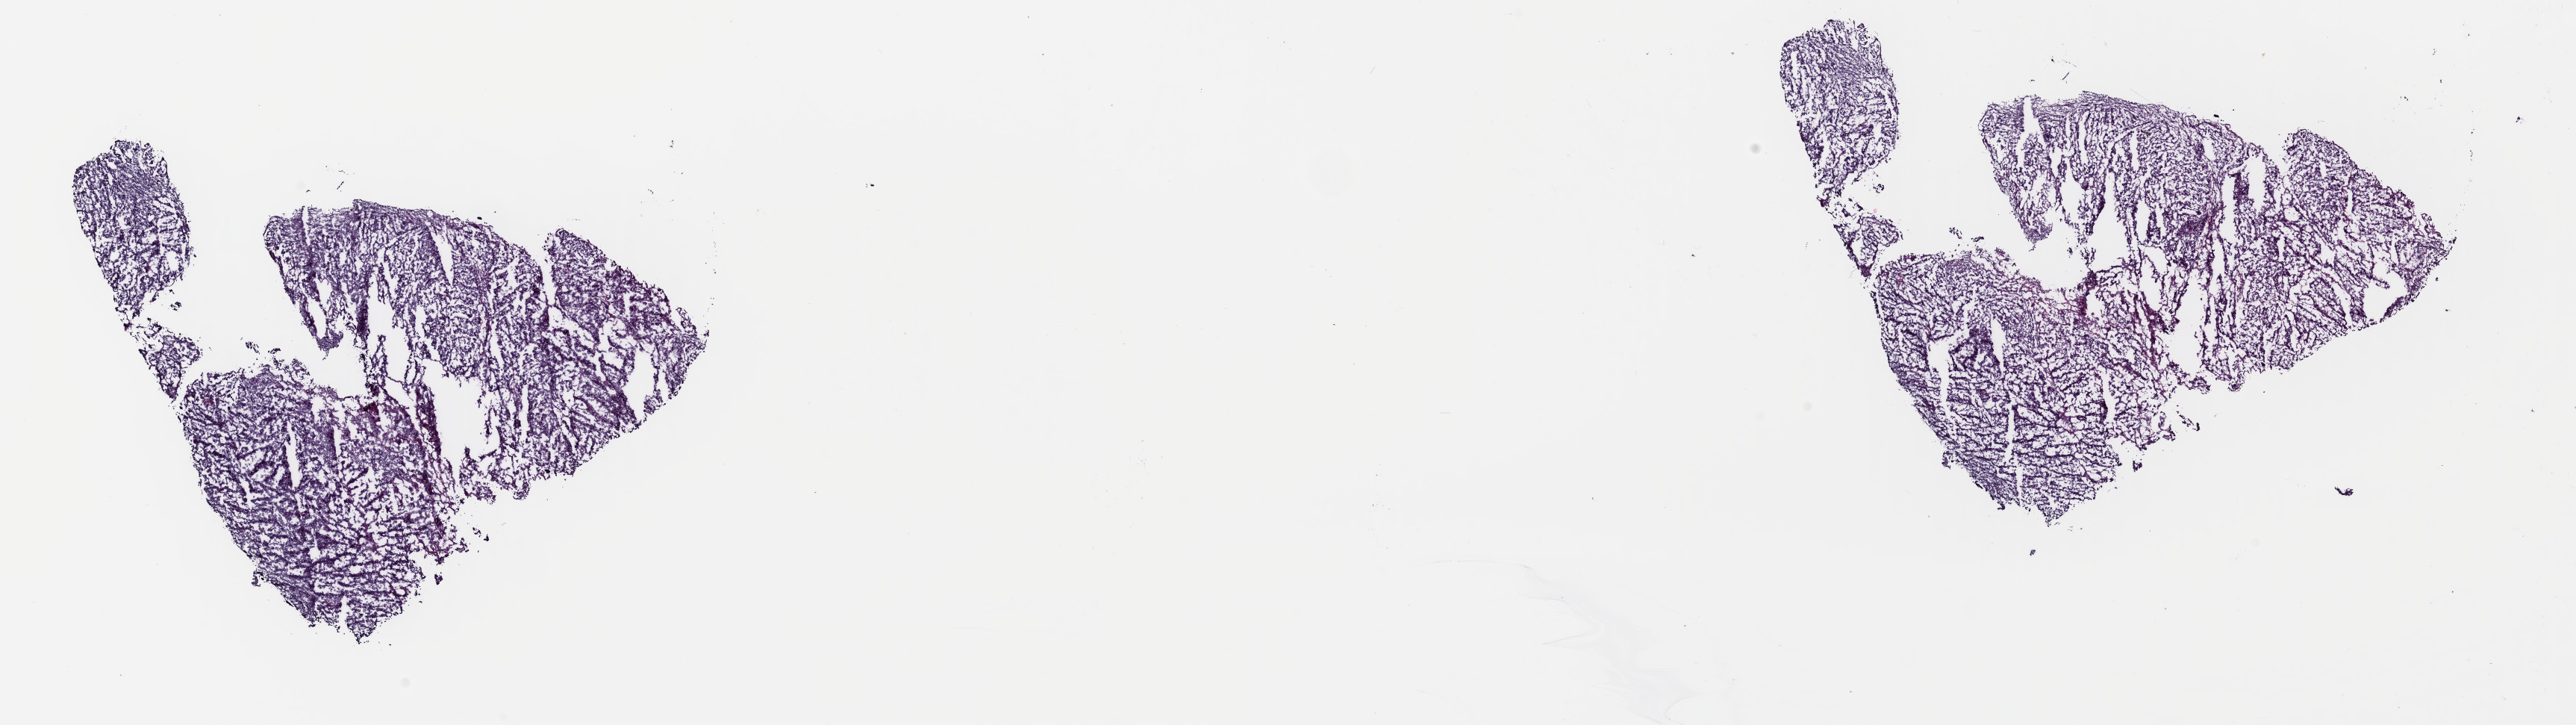
Whole-slide histology image, H&E-stained — low-resolution overview of the scanned area, about 27.3 x 7.7 mm; frozen section from the top of the tissue portion; uterus, primary tumour sample. Female patient; age at initial diagnosis 53 years. Histologic grade: G3 (poorly differentiated). Pathologist review of this section (percent, as recorded): tumour cells 95%, tumour nuclei 95%, normal cells 0%, stromal cells 0%, necrosis 5%. Inflammatory infiltration, as recorded: lymphocyte infiltration 1%, monocyte infiltration 2%, neutrophil infiltration 0%.
* FIGO stage: II
* histologic diagnosis: Endometrioid adenocarcinoma, NOS (endometrium)